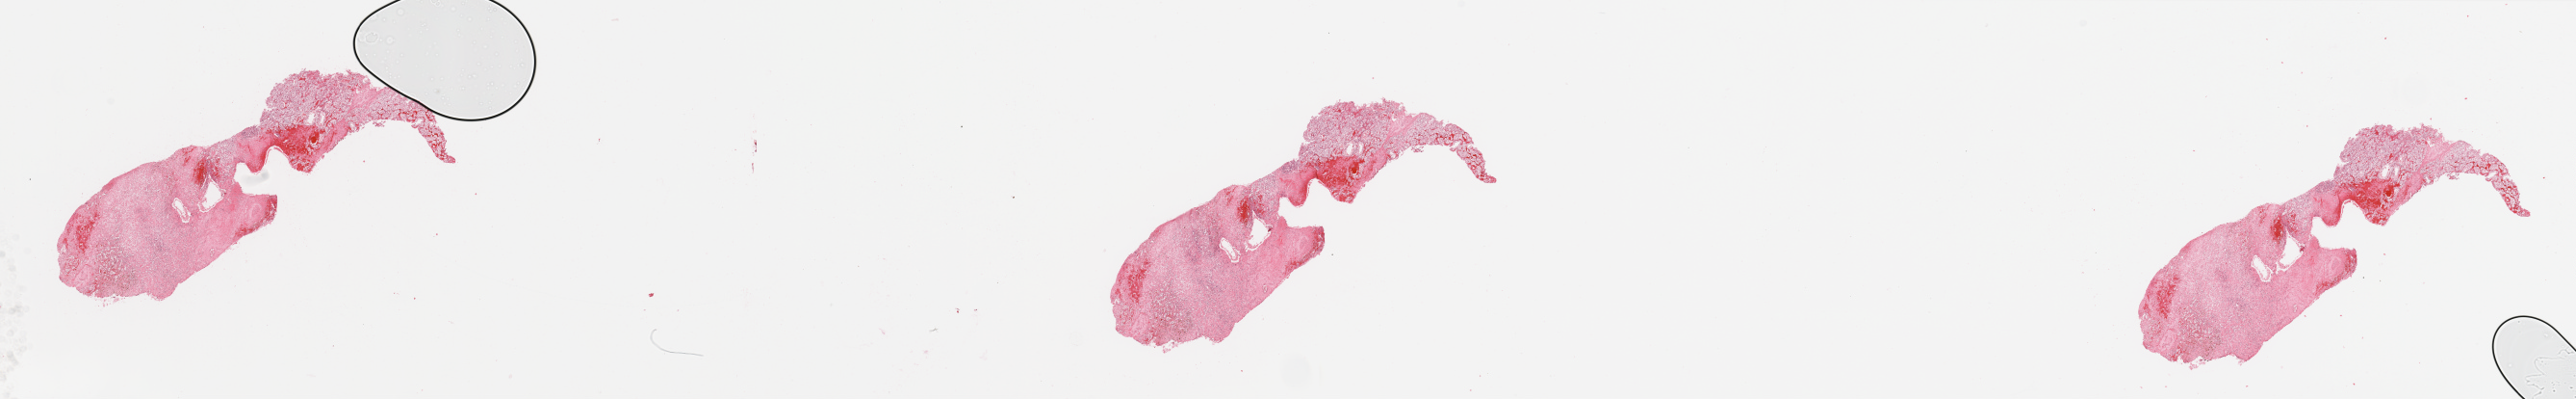
Whole-slide histology image, H&E, whole scanned area (about 42.3 x 6.5 mm, slide scanned at 20x) shown as a low-resolution overview. Tumour tissue sample, kidney. Male, 47 y/o. Histologic grade: G2 (moderately differentiated).
Histologic diagnosis: Renal cell carcinoma, NOS. Primary tumour site (as recorded): upper pole. AJCC pathologic stage: I.